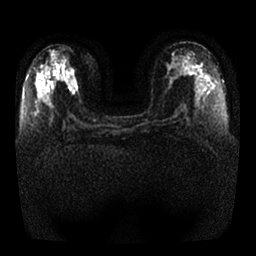
Breast MRI, one axial slice; slice 12 of 25 in the series (ordered by position); diffusion-weighted series; image 2 of 4 stored at this slice position (different b-values; order by instance number); 1.5 T; 256 × 256 image matrix, field of view 350 × 350 mm. Female patient.
Outlined on this slice (expert manual segmentation):
- tumour on diffusion-weighted imaging: box from (x=69, y=78) to (x=77, y=91) px